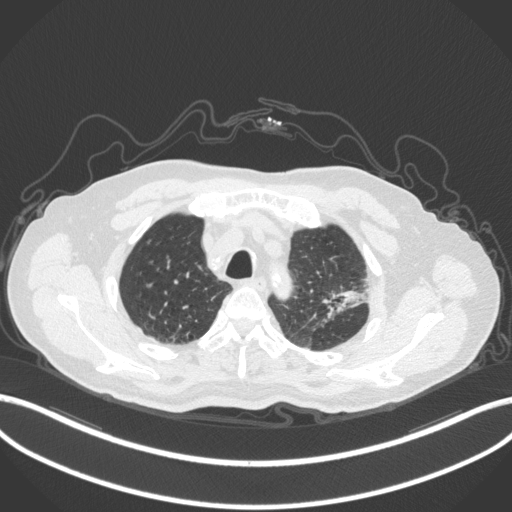
Chest CT, one axial slice. Slice 247 of 331 in the series (ordered by position). 120 kVp. Lung window (W 1500 / L -600 HU). 1 mm slice thickness. 512 × 512 image matrix, field of view 400 × 400 mm. Male patient, age 79 years. From the clinical record (not read from this slice): clinical TNM (as recorded): T2a N1 M1; histopathological grade: G3.
Annotated regions visible in this slice (bounding box drawn by a radiologist):
- lung tumour (recorded histology: adenocarcinoma): bounding box [x1, y1, x2, y2] px = [323, 283, 373, 325]